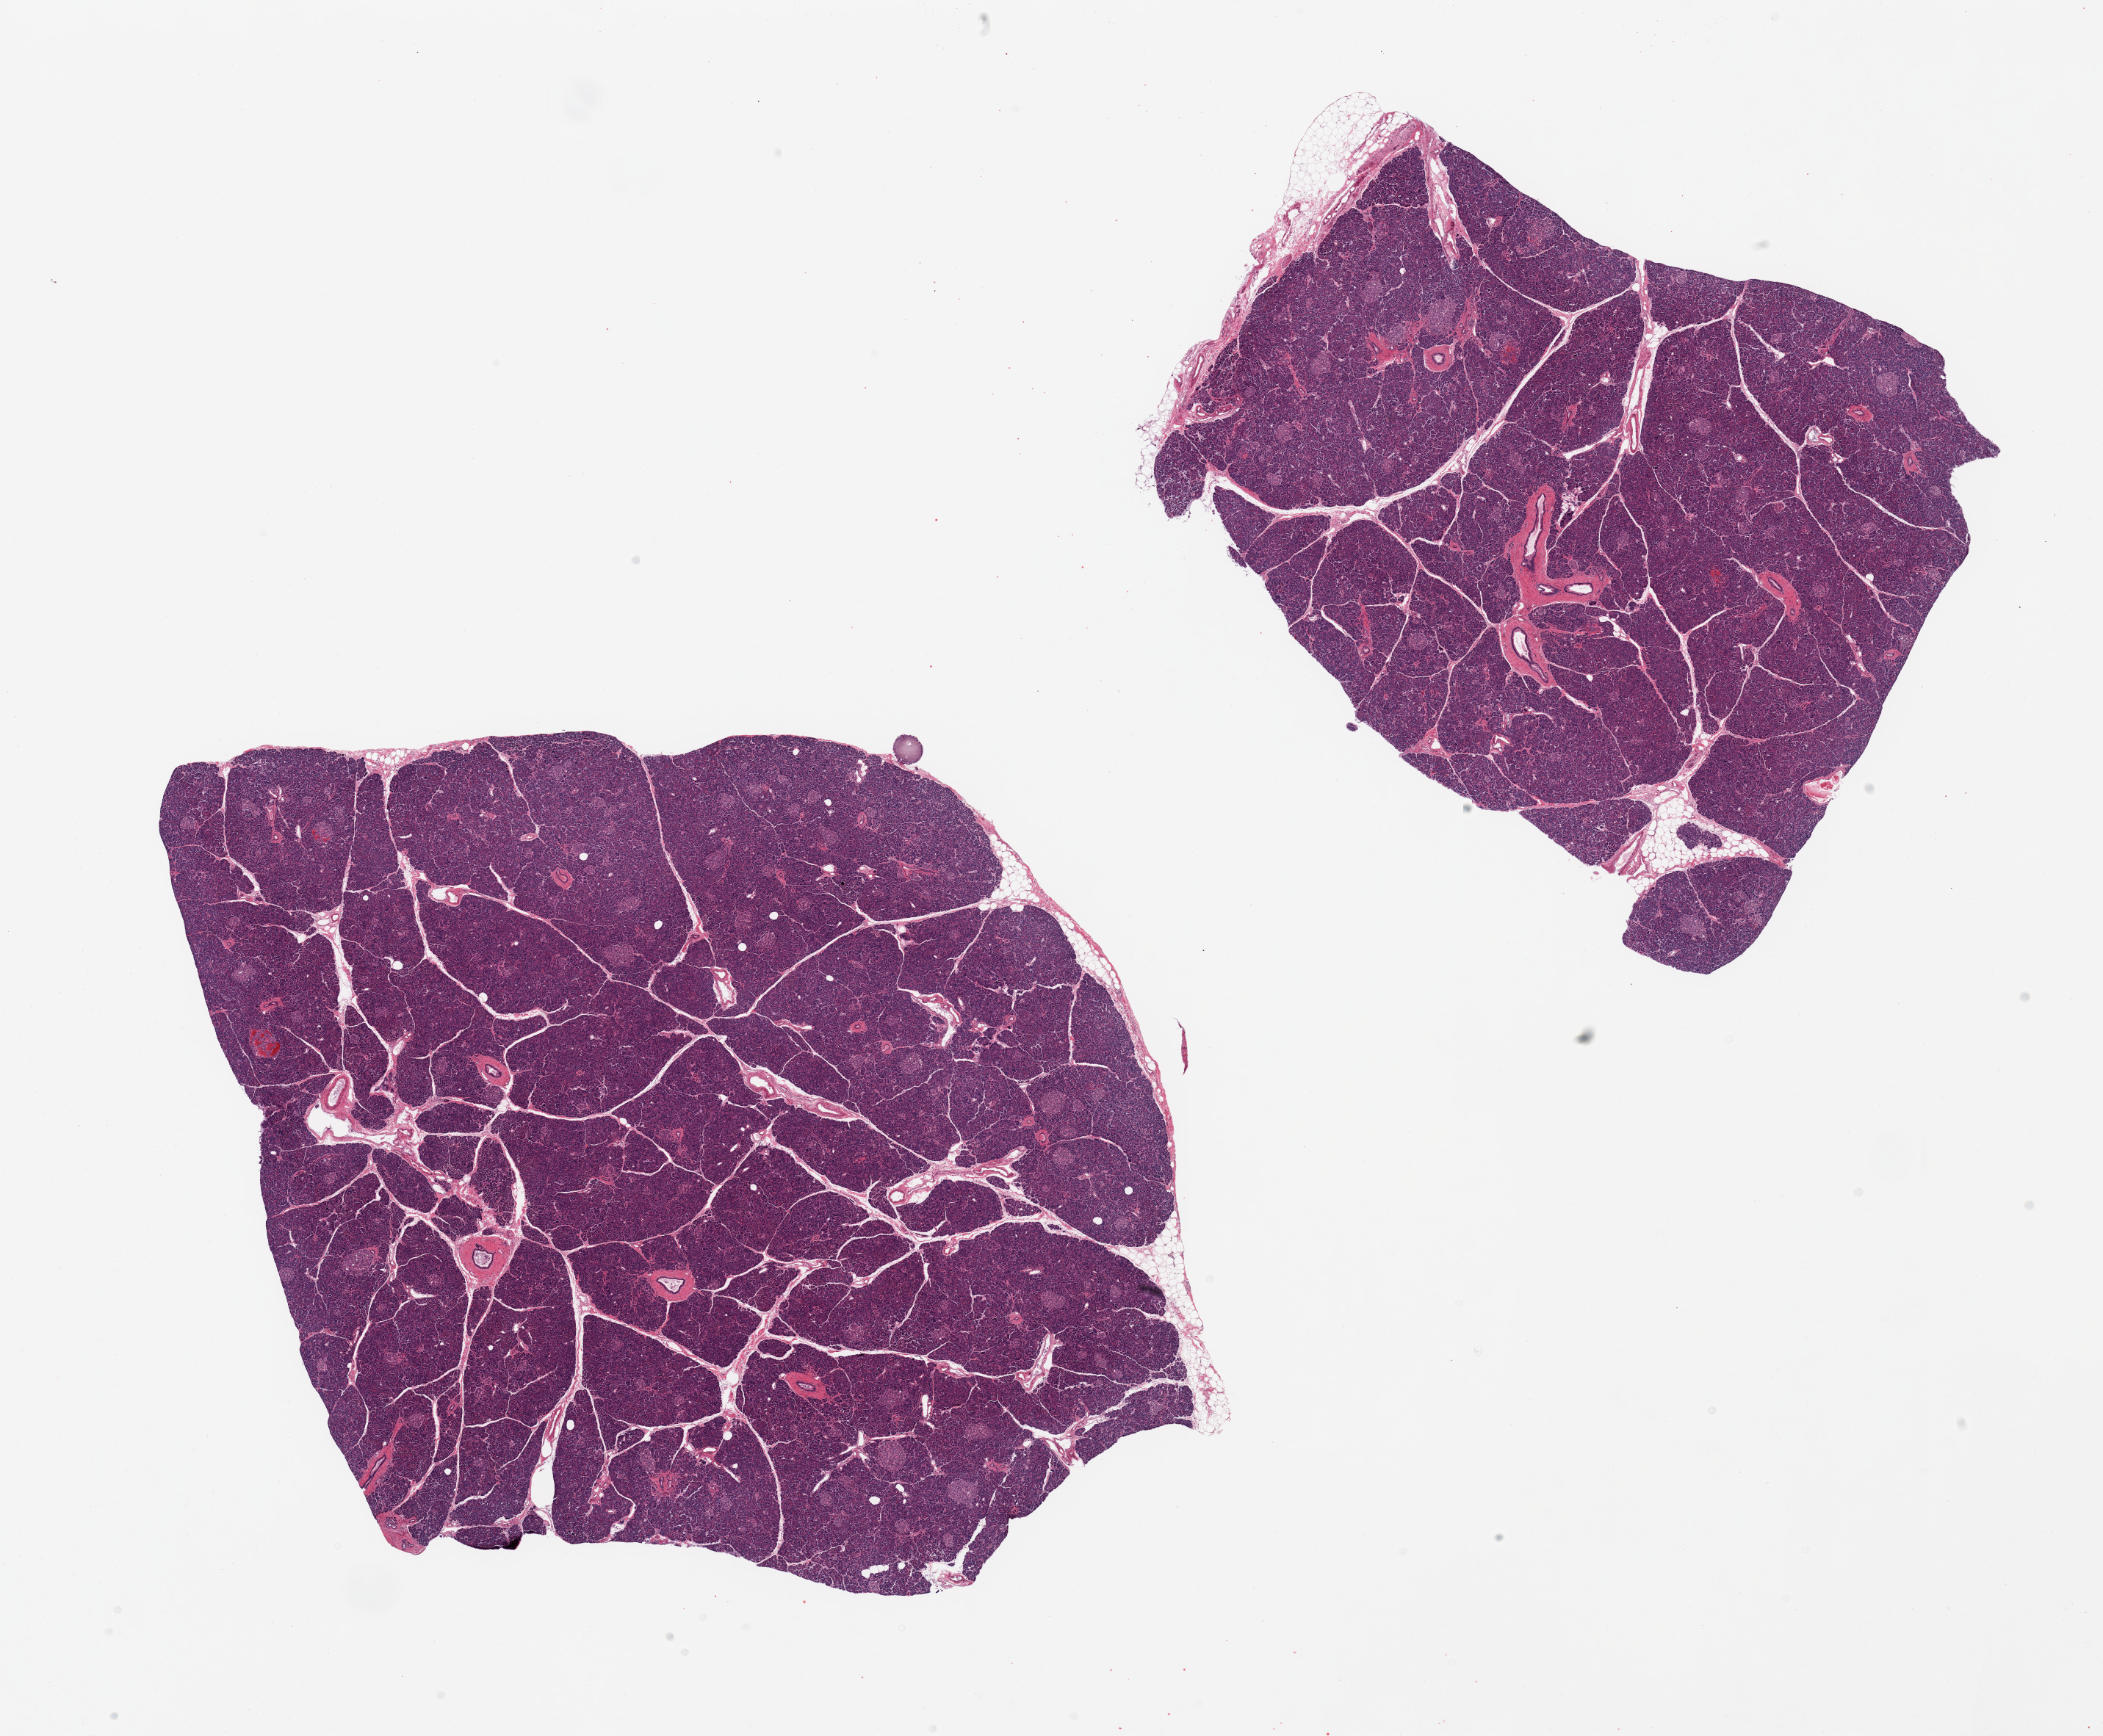
Whole-slide image, hematoxylin and eosin (H&E) stain — a low-resolution overview of the entire scanned area, about 22.6 x 18.7 mm (from a 20x scan). PAXgene-fixed paraffin-embedded (PFPE) section. Section of pancreas (target tissue). Donor tissue sample.
- pathologist's review note for this sample: 2 pieces; well preserved, islets well visualized